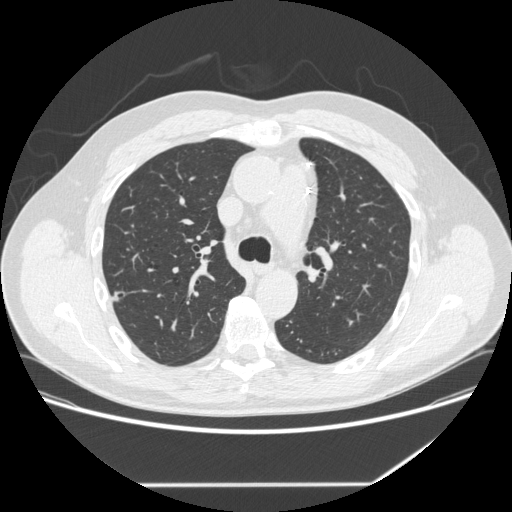
Low-dose screening chest CT, axial slice, first (baseline) screen, lung window (W 1500 / L -600 HU), 1.25 mm slice thickness, standard (soft-tissue) reconstruction kernel (STANDARD), slice 91 of 262 in the series, 512 × 512 image matrix. Male participant, aged 62 years at enrolment.
Expert reader's lesion annotation, bounding box (x1, y1, x2, y2) in pixels: (100, 280, 132, 312). Screening reader's record for this exam: no non-calcified nodule ≥4 mm recorded.